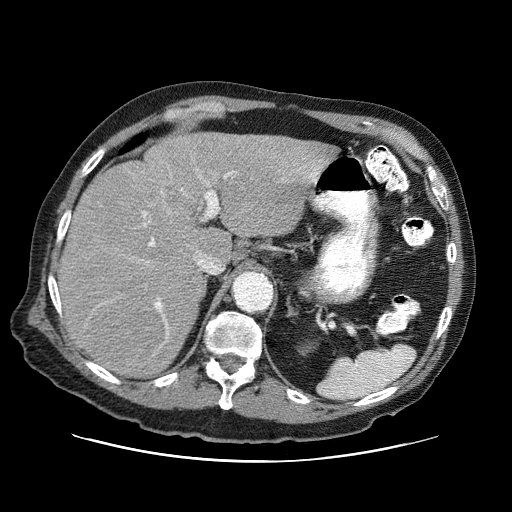
Contrast-enhanced abdominal CT (liver protocol), one axial slice; position 50 of 87 along the scan axis; reconstruction kernel STANDARD; one of 3 acquisitions stored at this slice position; soft-tissue window (W 400 / L 40 HU); 2.5 mm slice thickness; 512 × 512 image matrix, field of view 400 × 400 mm. Case-level facts recorded for this patient, not image findings: diagnosis: hepatocellular carcinoma (patient treated with transarterial chemoembolisation; whether this scan precedes or follows treatment is not stated here); TNM stage (as recorded): Stage-IIIA; Child-Pugh class: A; tumour differentiation: well differentiated; tumour size: 6 cm.
Annotated regions visible in this slice (semi-automatic segmentation, software-assisted and operator-edited):
- abdominal aorta: bounding box <234,272,272,310> (left, top, right, bottom; pixels)
- liver parenchyma outside the tumour (the mass and vessels are separate outlines, so this box may not span the whole liver): <58,132,332,376>
- liver vessels: <140,170,318,334>